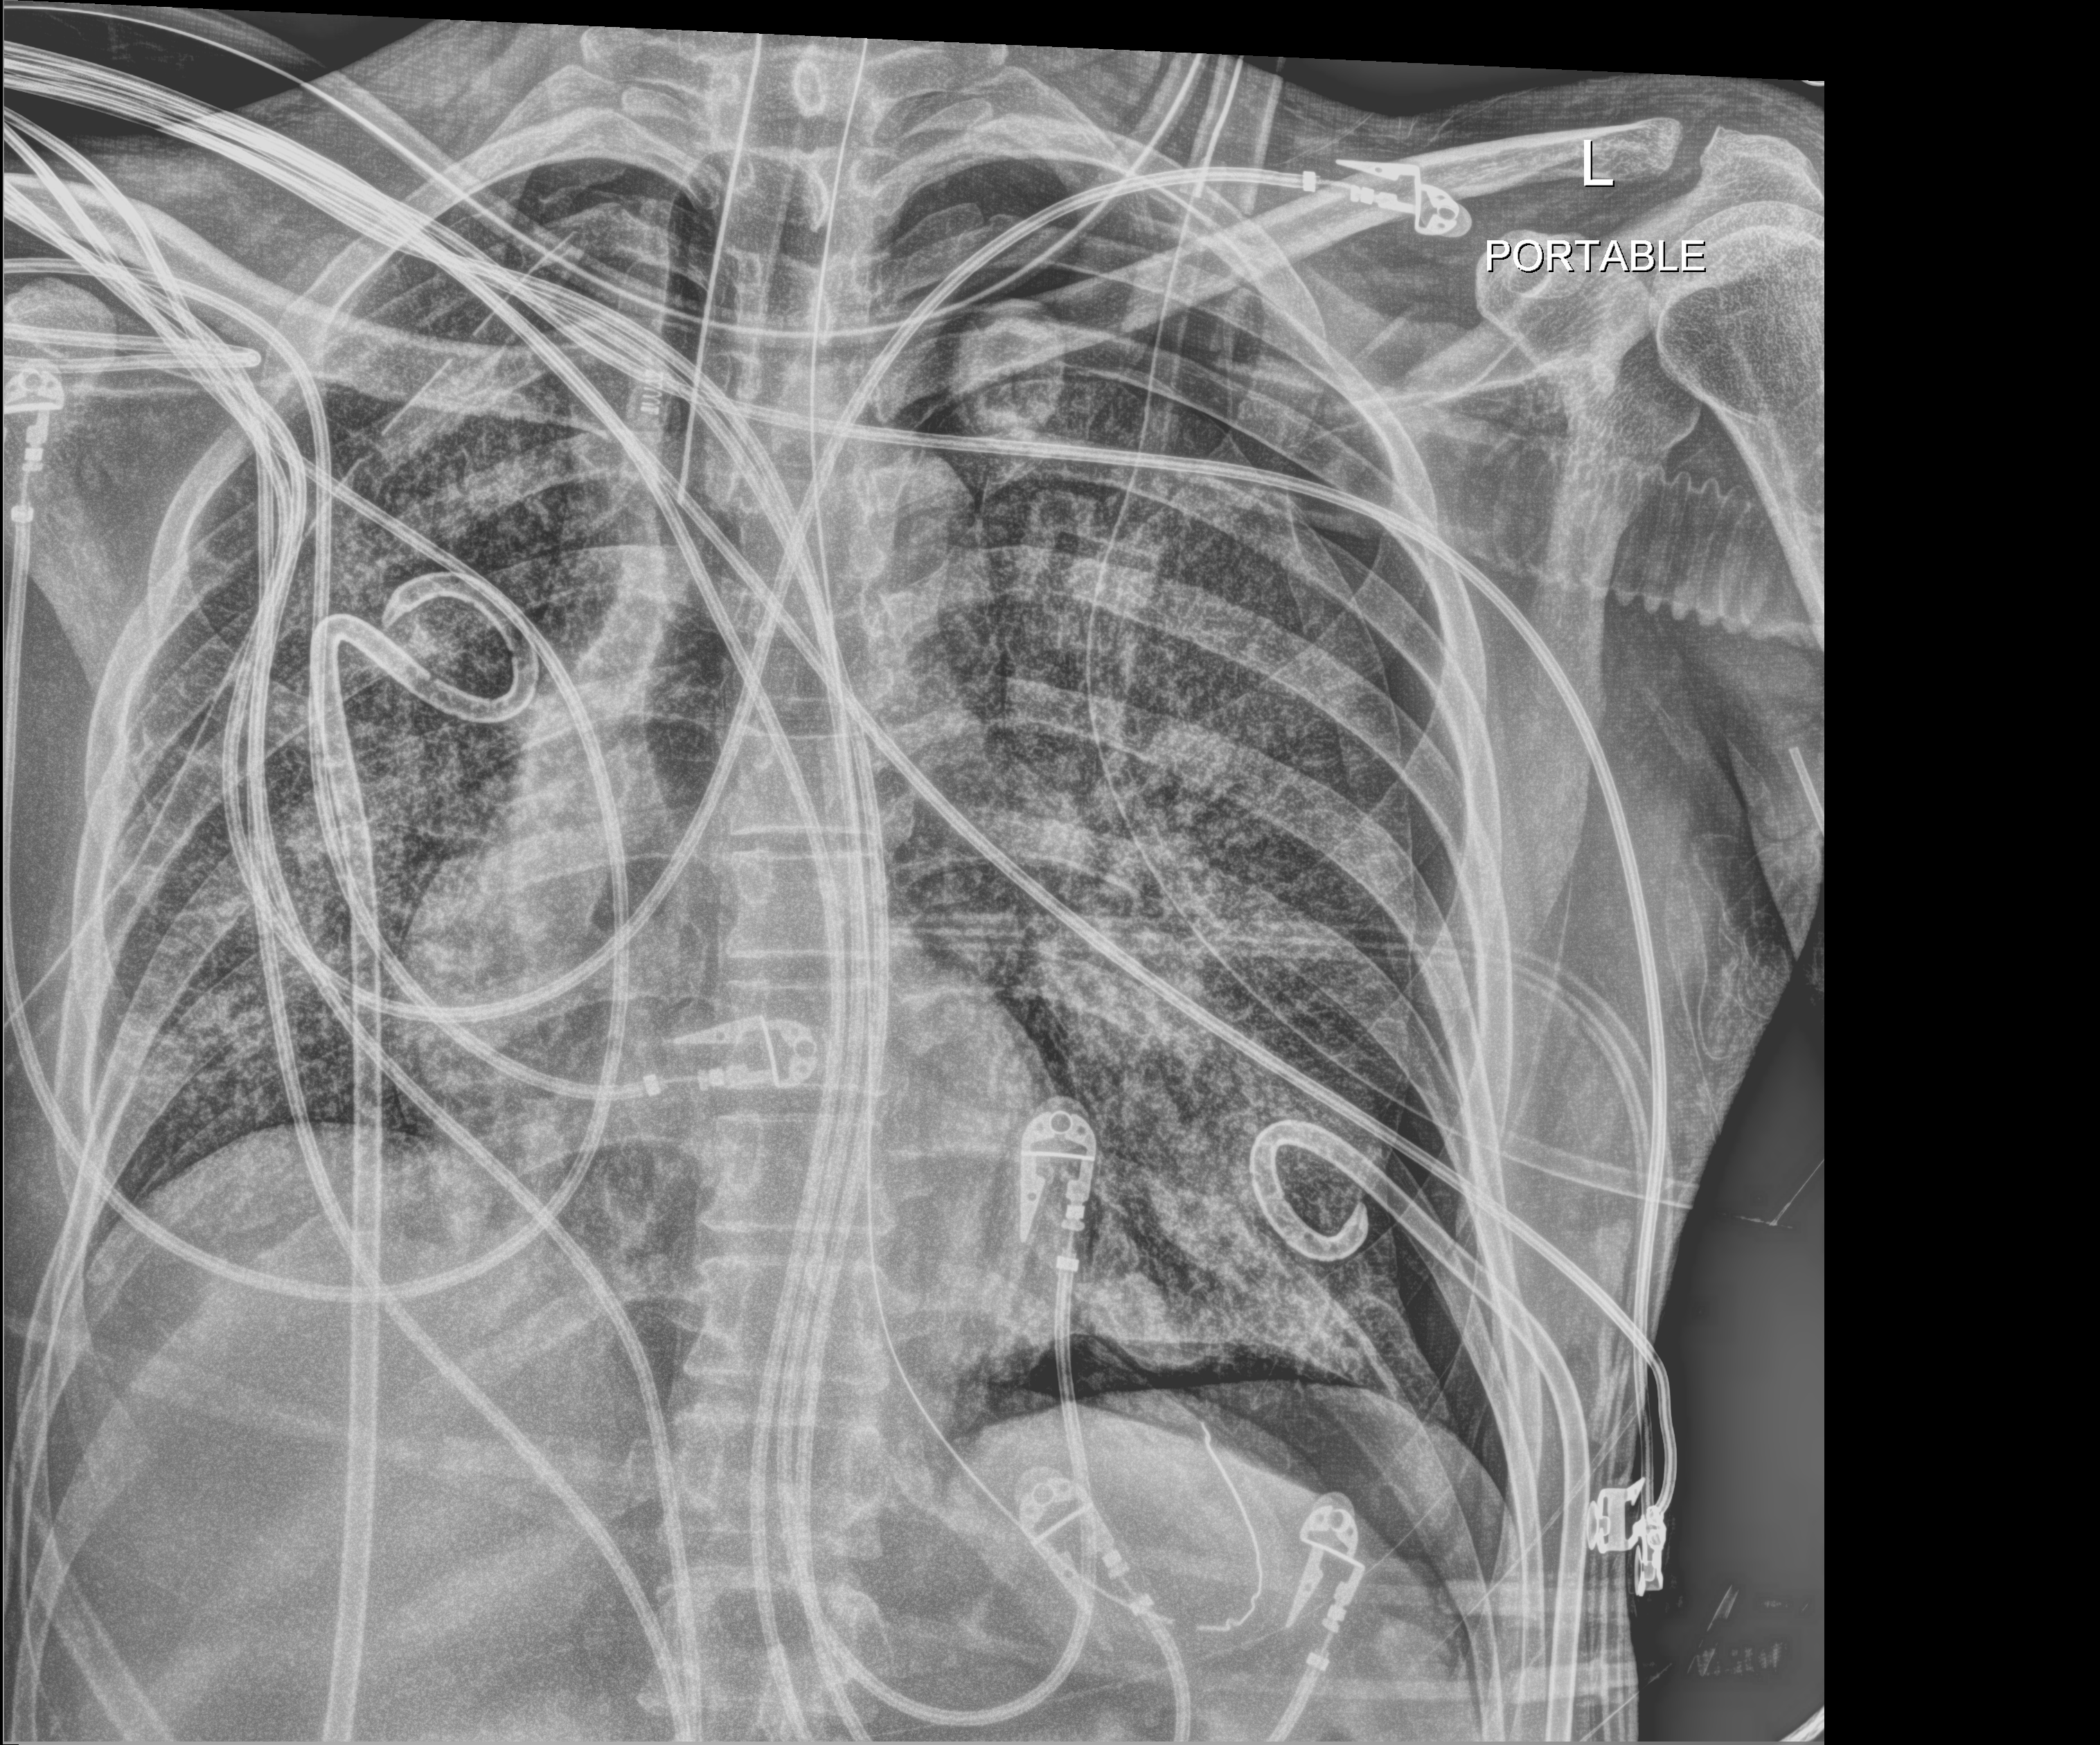
Chest radiograph. Adult patient hospitalised with COVID-19, age 18–59 years.
Admission-level facts for this patient (not findings on this image; timing relative to this image not recorded): admitted to intensive care during this hospital stay: yes; smoking status (admission record): never.